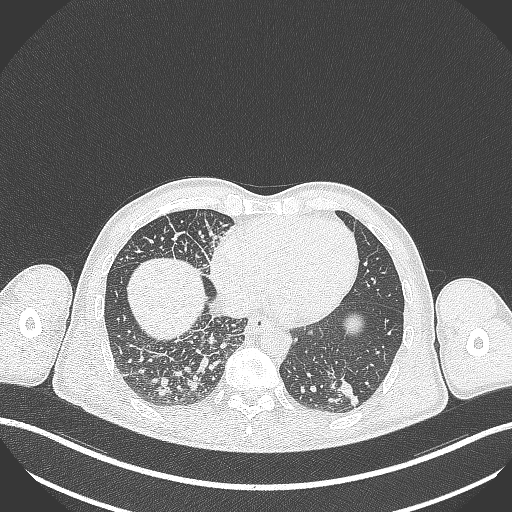
Chest CT, one axial slice. Slice 89 of 348 in the series (ordered by position). Reconstruction kernel B70f. 120 kVp. Lung window (W 1500 / L -600 HU). 512 × 512 image matrix, field of view 400 × 400 mm. Male patient, age 49 years. Case-level facts recorded for this patient, not image findings: clinical TNM (as recorded): T2b N1 M0.
Structures marked on this image (rectangle marked by the reading radiologist):
- lung tumour (recorded histology: adenocarcinoma): box from (x=327, y=369) to (x=365, y=410) px